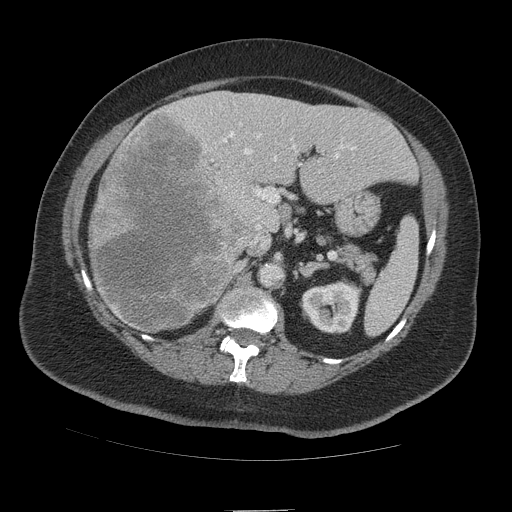
Contrast-enhanced abdominal CT (liver protocol), one axial slice; reconstruction kernel STANDARD; 140 kVp; soft-tissue window (W 400 / L 40 HU); 2.5 mm slice thickness; 512 × 512 image matrix, field of view 420 × 420 mm. From the clinical record (not read from this slice): diagnosis: hepatocellular carcinoma (patient treated with transarterial chemoembolisation; whether this scan precedes or follows treatment is not stated here); TNM stage (as recorded): Stage-IVB; Child-Pugh class: A; tumour nodularity: multinodular.
Structures marked on this image (semi-automatic segmentation, software-assisted and operator-edited):
- liver parenchyma outside the tumour (the mass and vessels are separate outlines, so this box may not span the whole liver): bounding box (x1, y1, x2, y2) in pixels: (90, 90, 416, 320)
- mass: (88, 111, 253, 333)
- liver vessels: (205, 131, 356, 242)